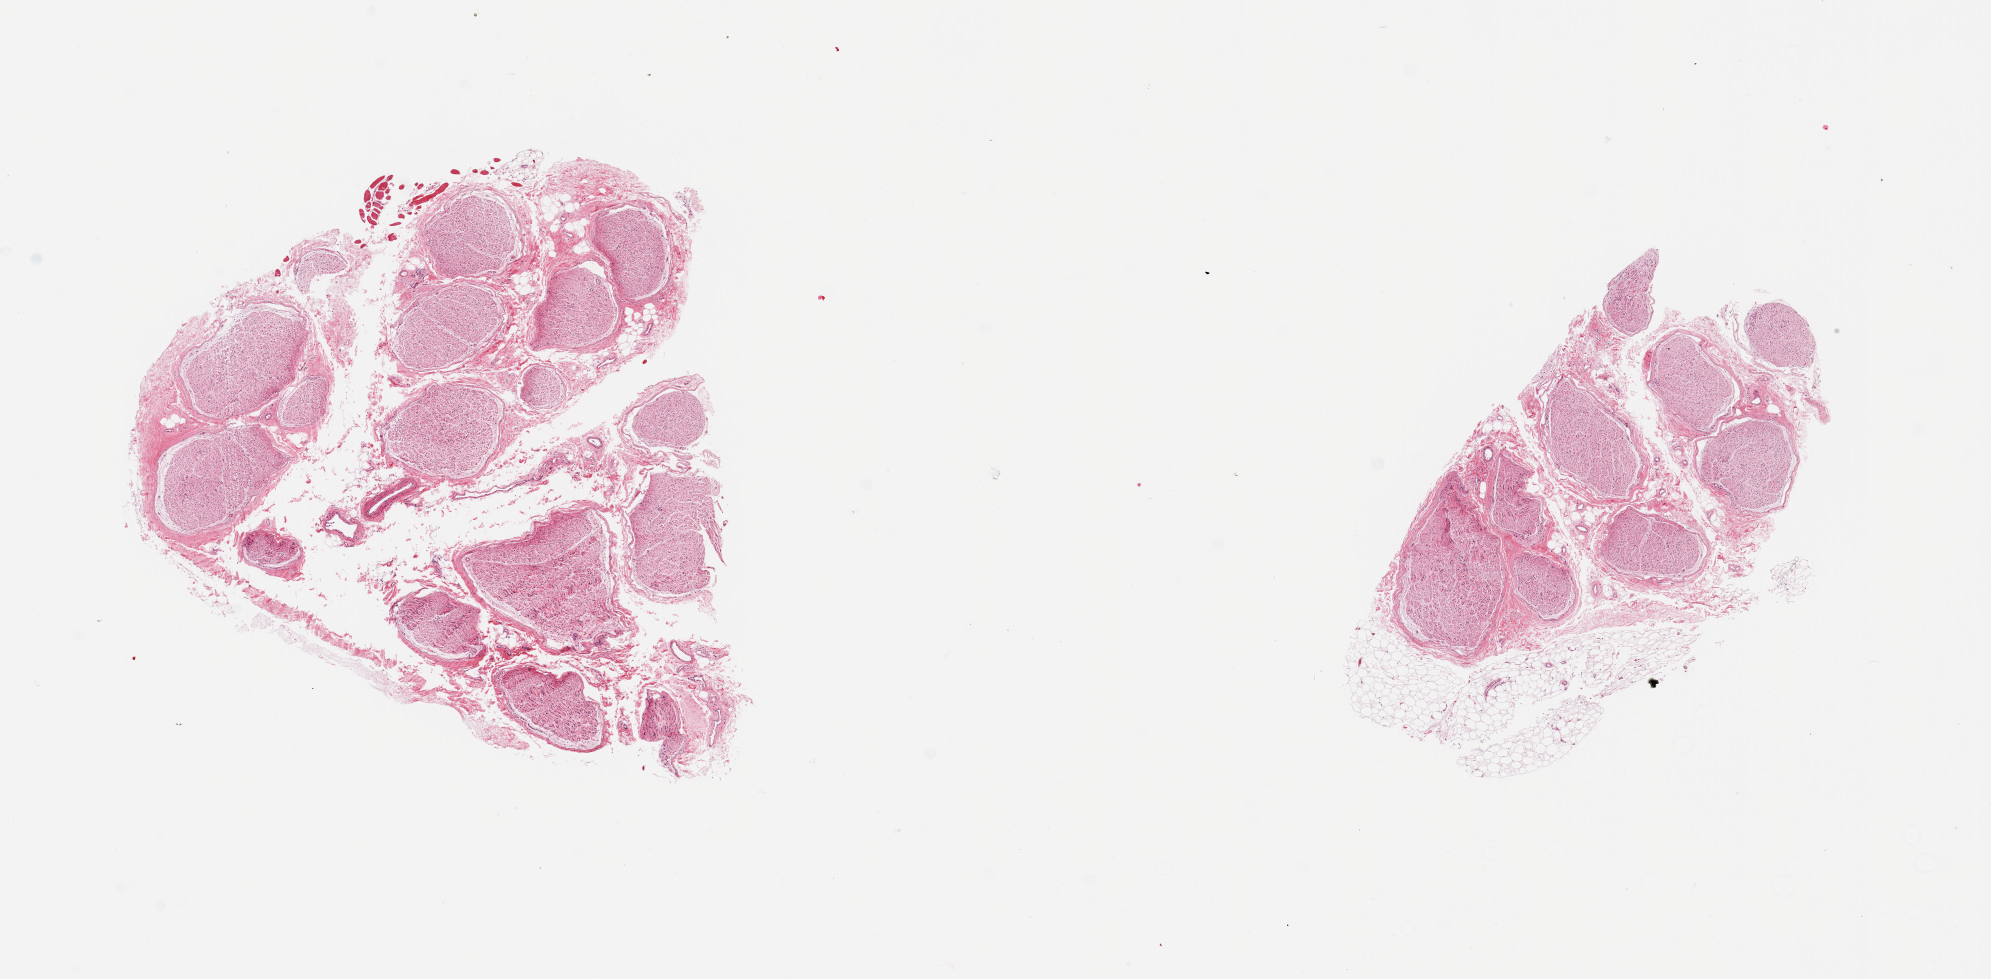
Digitized haematoxylin and eosin-stained section, whole scanned area (about 15.8 x 7.7 mm) shown as a low-resolution overview; PAXgene-fixed, paraffin-embedded tissue; sampled site (target tissue): tibial nerve; tissue donor sample. Female donor.
Review note (as recorded): 2 pieces; 10% internall fatty tissue.